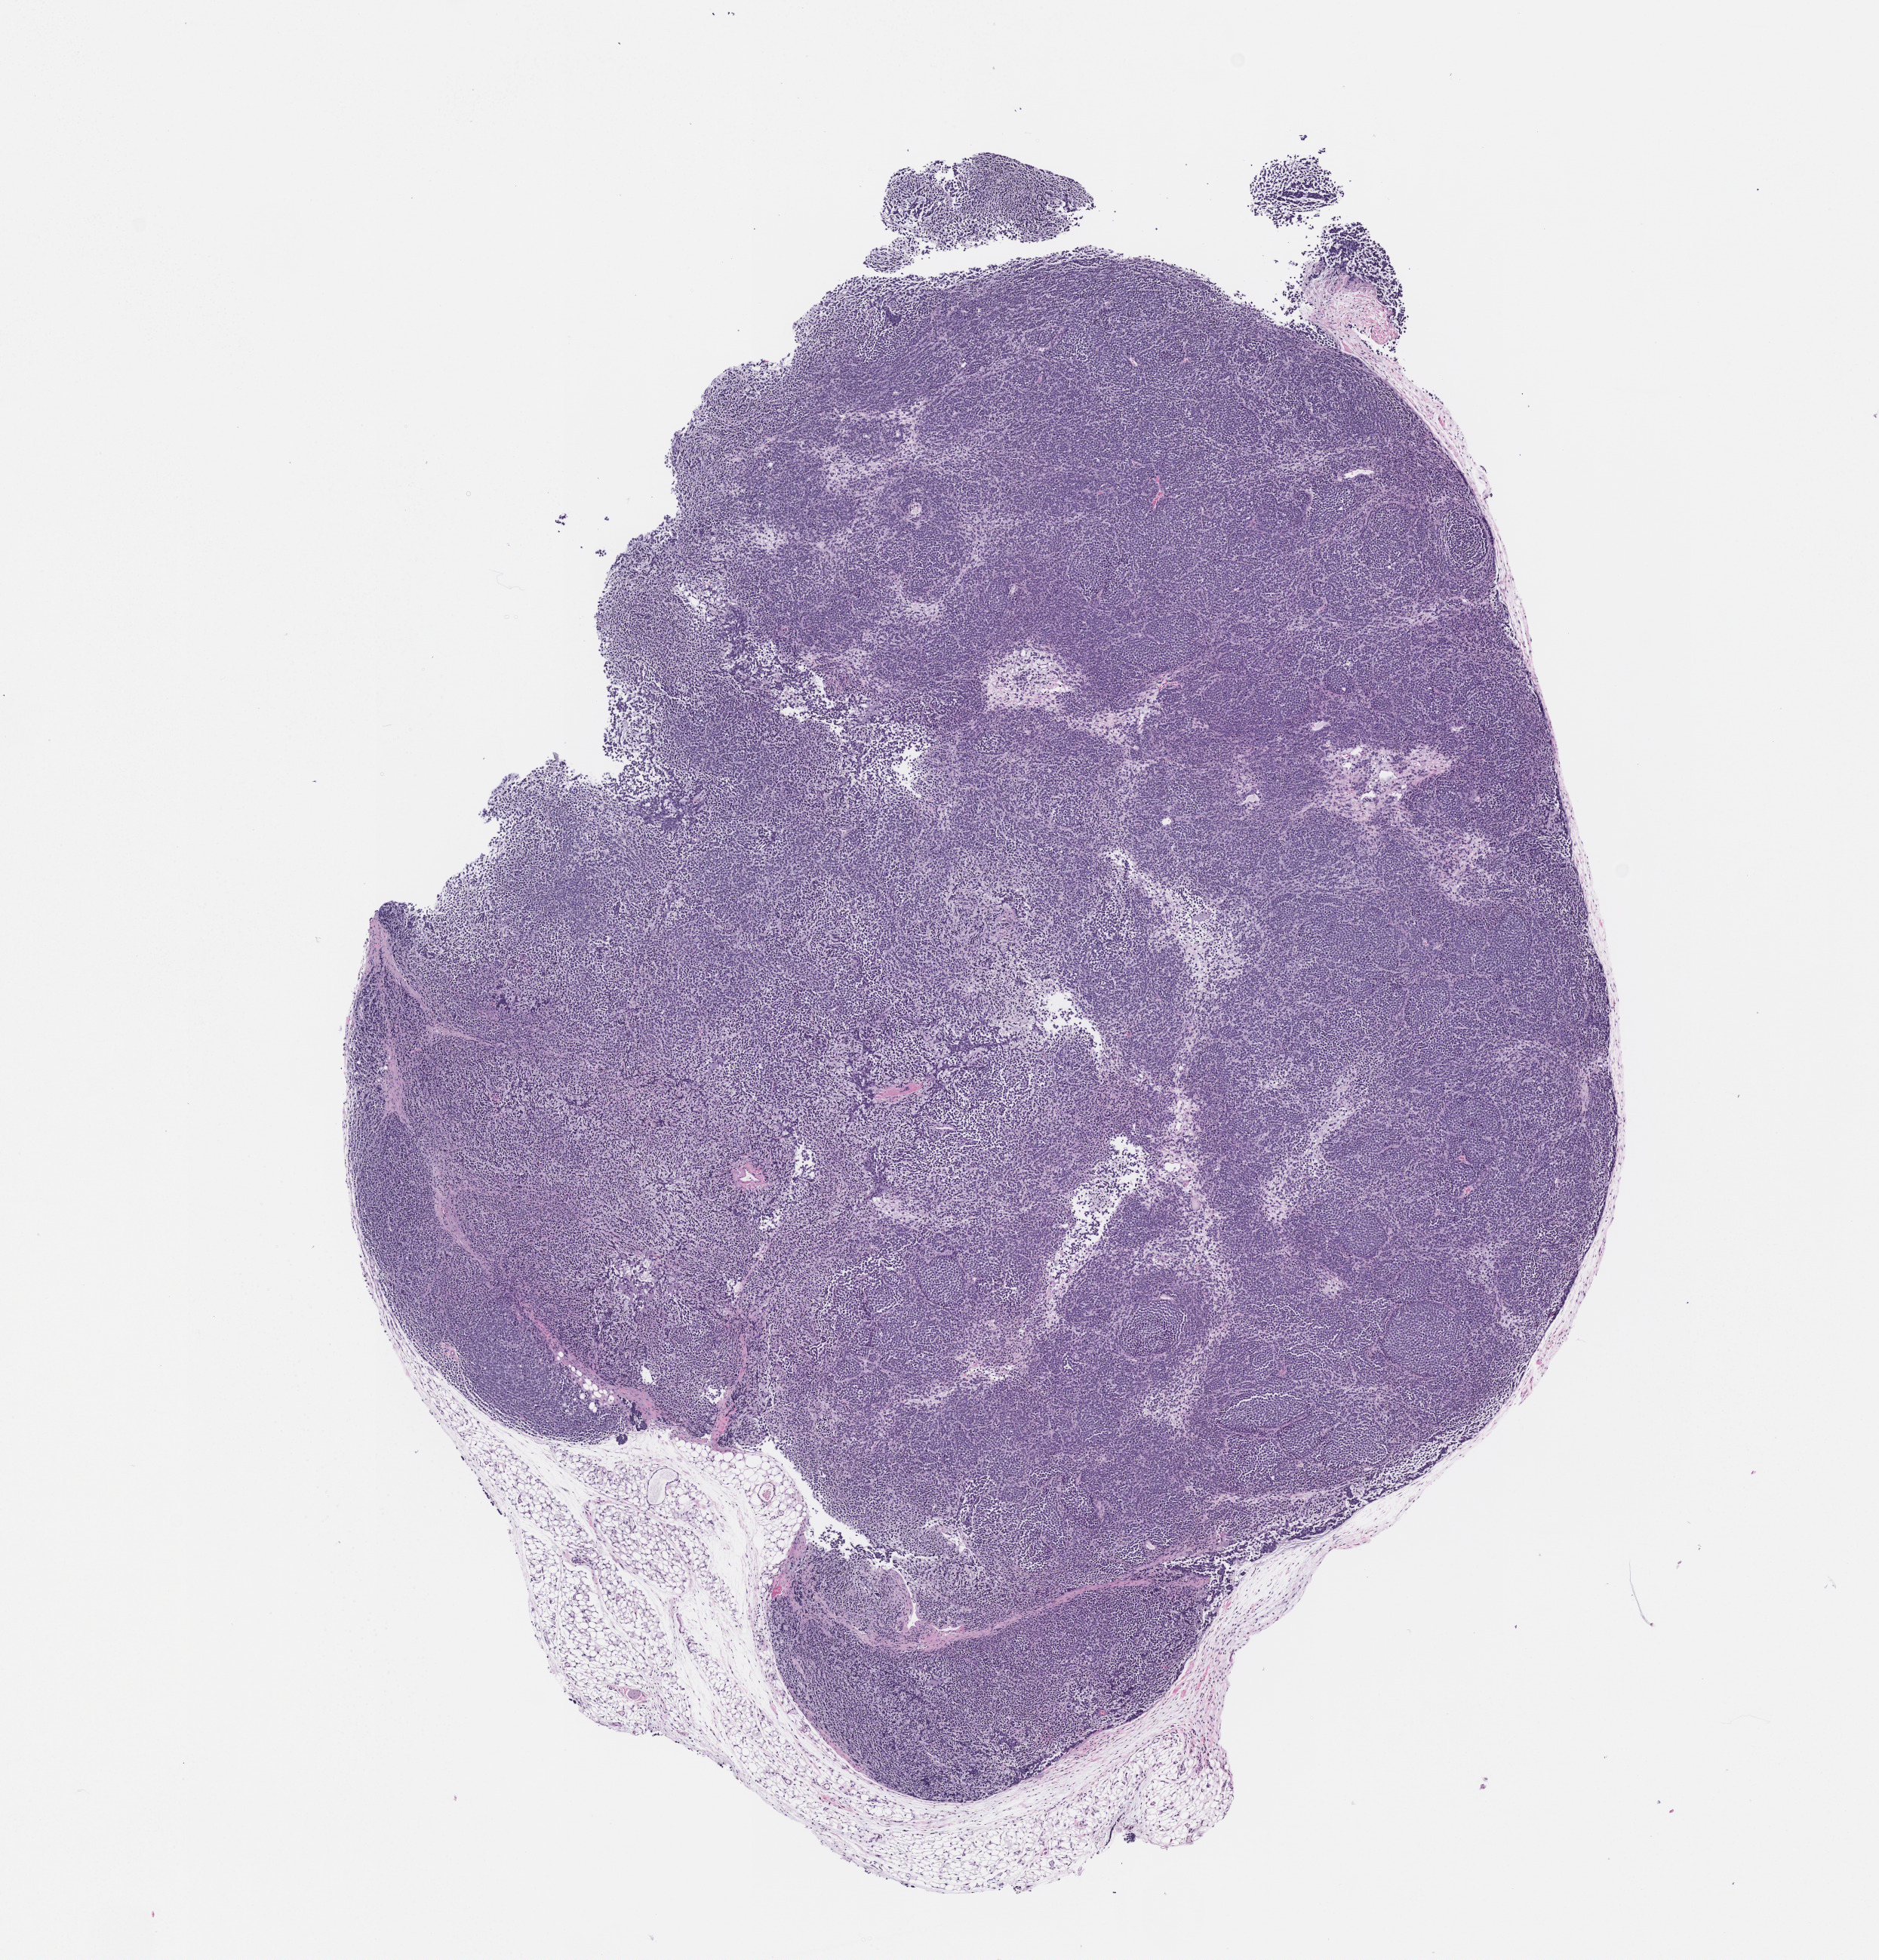
Whole-slide image, H&E: patient-derived xenograft (human tumor grown in a mouse), passage 1 — a low-resolution overview of the entire scanned area, about 10.0 x 10.4 mm; formalin-fixed, paraffin-embedded (FFPE) tissue; originating tumor site category: endocrine.
Originating patient diagnosis: Merkel Cell Carcinoma.